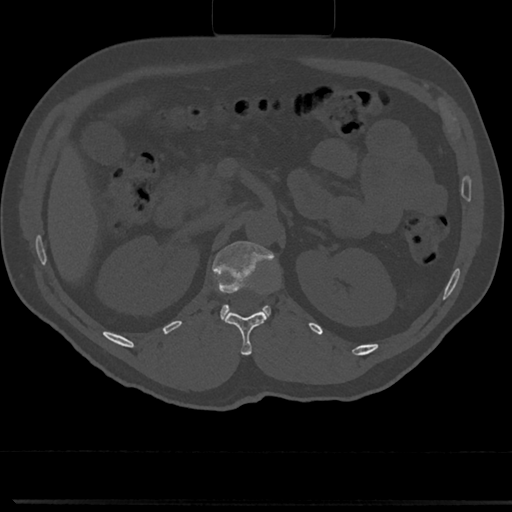
CT including the spine, one axial slice. Position 114 of 817 along the scan axis. Reconstruction kernel Br40s/3. 120 kVp. Bone window (W 1800 / L 400 HU). 0.5 mm slice thickness. 512 × 512 image matrix, field of view 355 × 355 mm. Male patient, age 61 years. Case-level facts recorded for this patient, not image findings: primary cancer: prostate.
Structures marked on this image (semi-automatically segmented with operator editing):
- L1 vertebra: bounding box (x1, y1, x2, y2) in pixels: (212, 240, 278, 325)
- T12 vertebra: (223, 310, 268, 355)